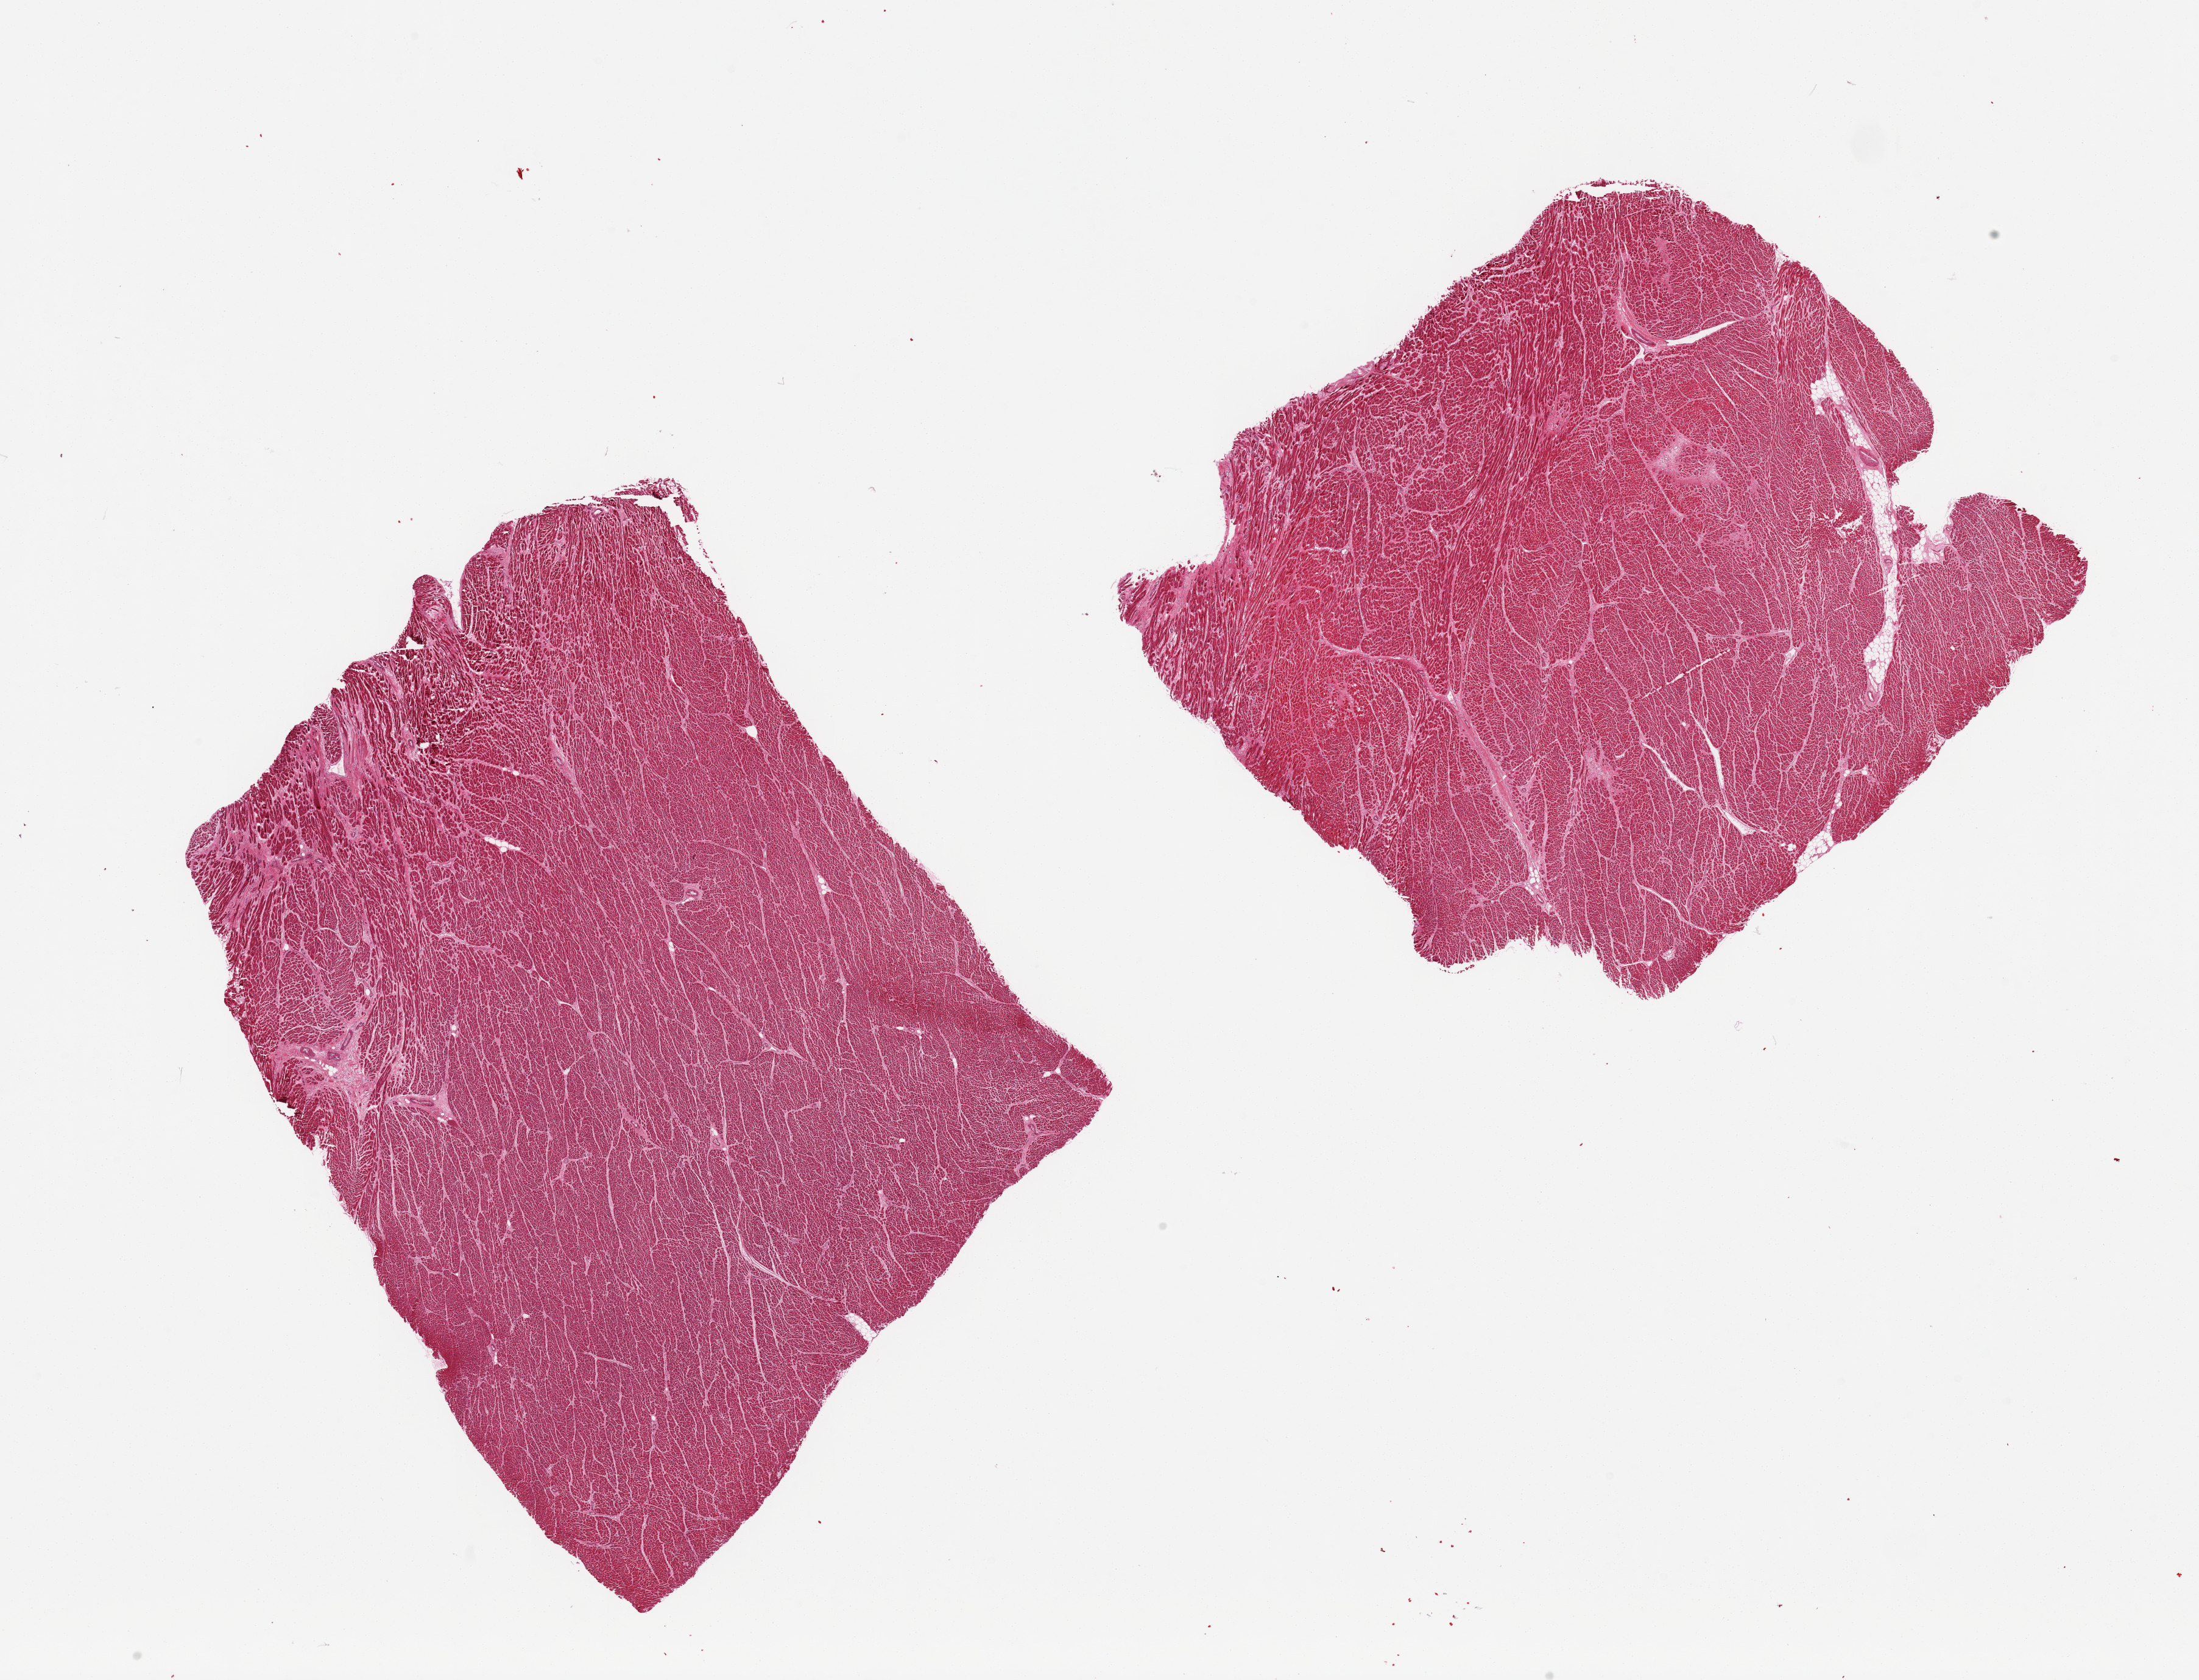
Whole-slide image, H&E stain, brightfield — shown as a low-resolution overview of the whole scanned area (about 28.5 x 21.8 mm); PAXgene-fixed paraffin-embedded (PFPE) section; sampled site (target tissue): heart; tissue donor sample. Donor sex: male.
Review note (as recorded): 2 pieces, interstitial and patchy fibrosis.